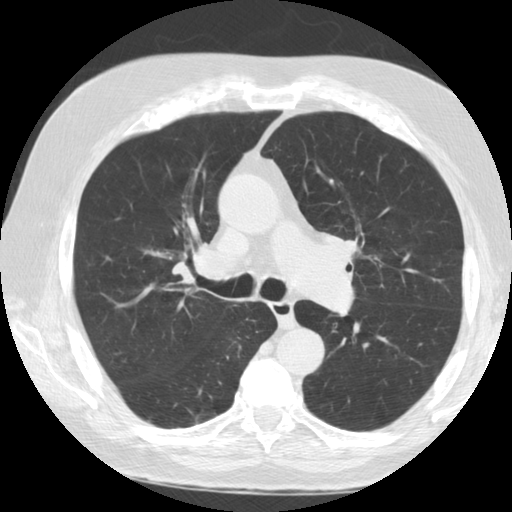
Chest CT (low-dose screening protocol), one axial image, second annual screen, lung window (W 1500 / L -600 HU), 2.5 mm slice thickness, standard (soft-tissue) reconstruction kernel (STANDARD). Male participant, aged 72 years at enrolment. Former smoker at enrolment.
Expert-annotated lung lesion, bounding box <162,222,231,293> (left, top, right, bottom; pixels). No non-calcified nodule or mass ≥4 mm was recorded by the screening reader at this exam. Official screen result: negative screen, minor abnormalities not suspicious for lung cancer. Lung cancer was diagnosed 415 days after this screen (after the third annual screen): small cell carcinoma, NOS, right upper lobe, stage IV (AJCC 6th edition), 7 mm at pathology.